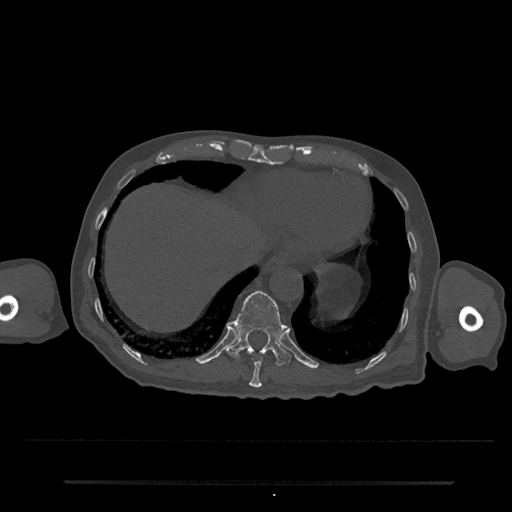
CT including the spine, one axial slice; position 272 of 797 along the scan axis; 120 kVp; bone window (W 1800 / L 400 HU); 0.5 mm slice thickness; 512 × 512 image matrix, field of view 427 × 427 mm. Patient: male, 74 years. From the clinical record (not read from this slice): primary cancer: prostate.
Outlined on this slice (semi-automatically segmented with operator editing):
- T10 vertebra: bounding box [x1, y1, x2, y2] px = [249, 357, 263, 388]
- T11 vertebra: [227, 290, 291, 366]